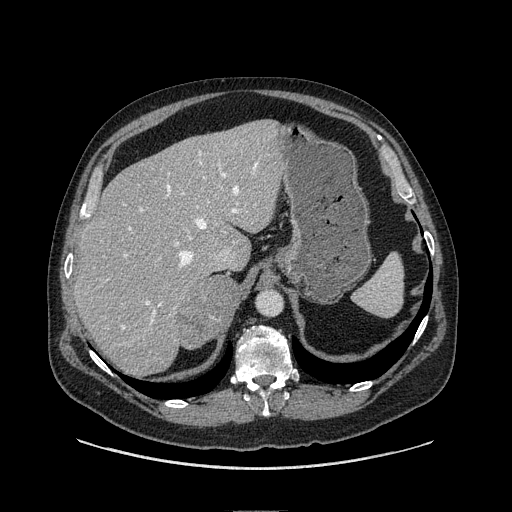
Contrast-enhanced abdominal CT, one axial slice. Position 80 of 149 along the scan axis. Soft-tissue window (W 400 / L 40 HU). 1.25 mm slice thickness. 512 × 512 image matrix, field of view 440 × 440 mm. Male patient. From the clinical record (not read from this slice): diagnosis: adrenocortical carcinoma; tumour side: right adrenal; tumour size at pathology: 7.5 cm; Ki-67 index: 15 %; stage (as recorded): 2.
Annotated regions visible in this slice (semi-automatically segmented with operator editing):
- mass: box from (x=182, y=275) to (x=241, y=348) px